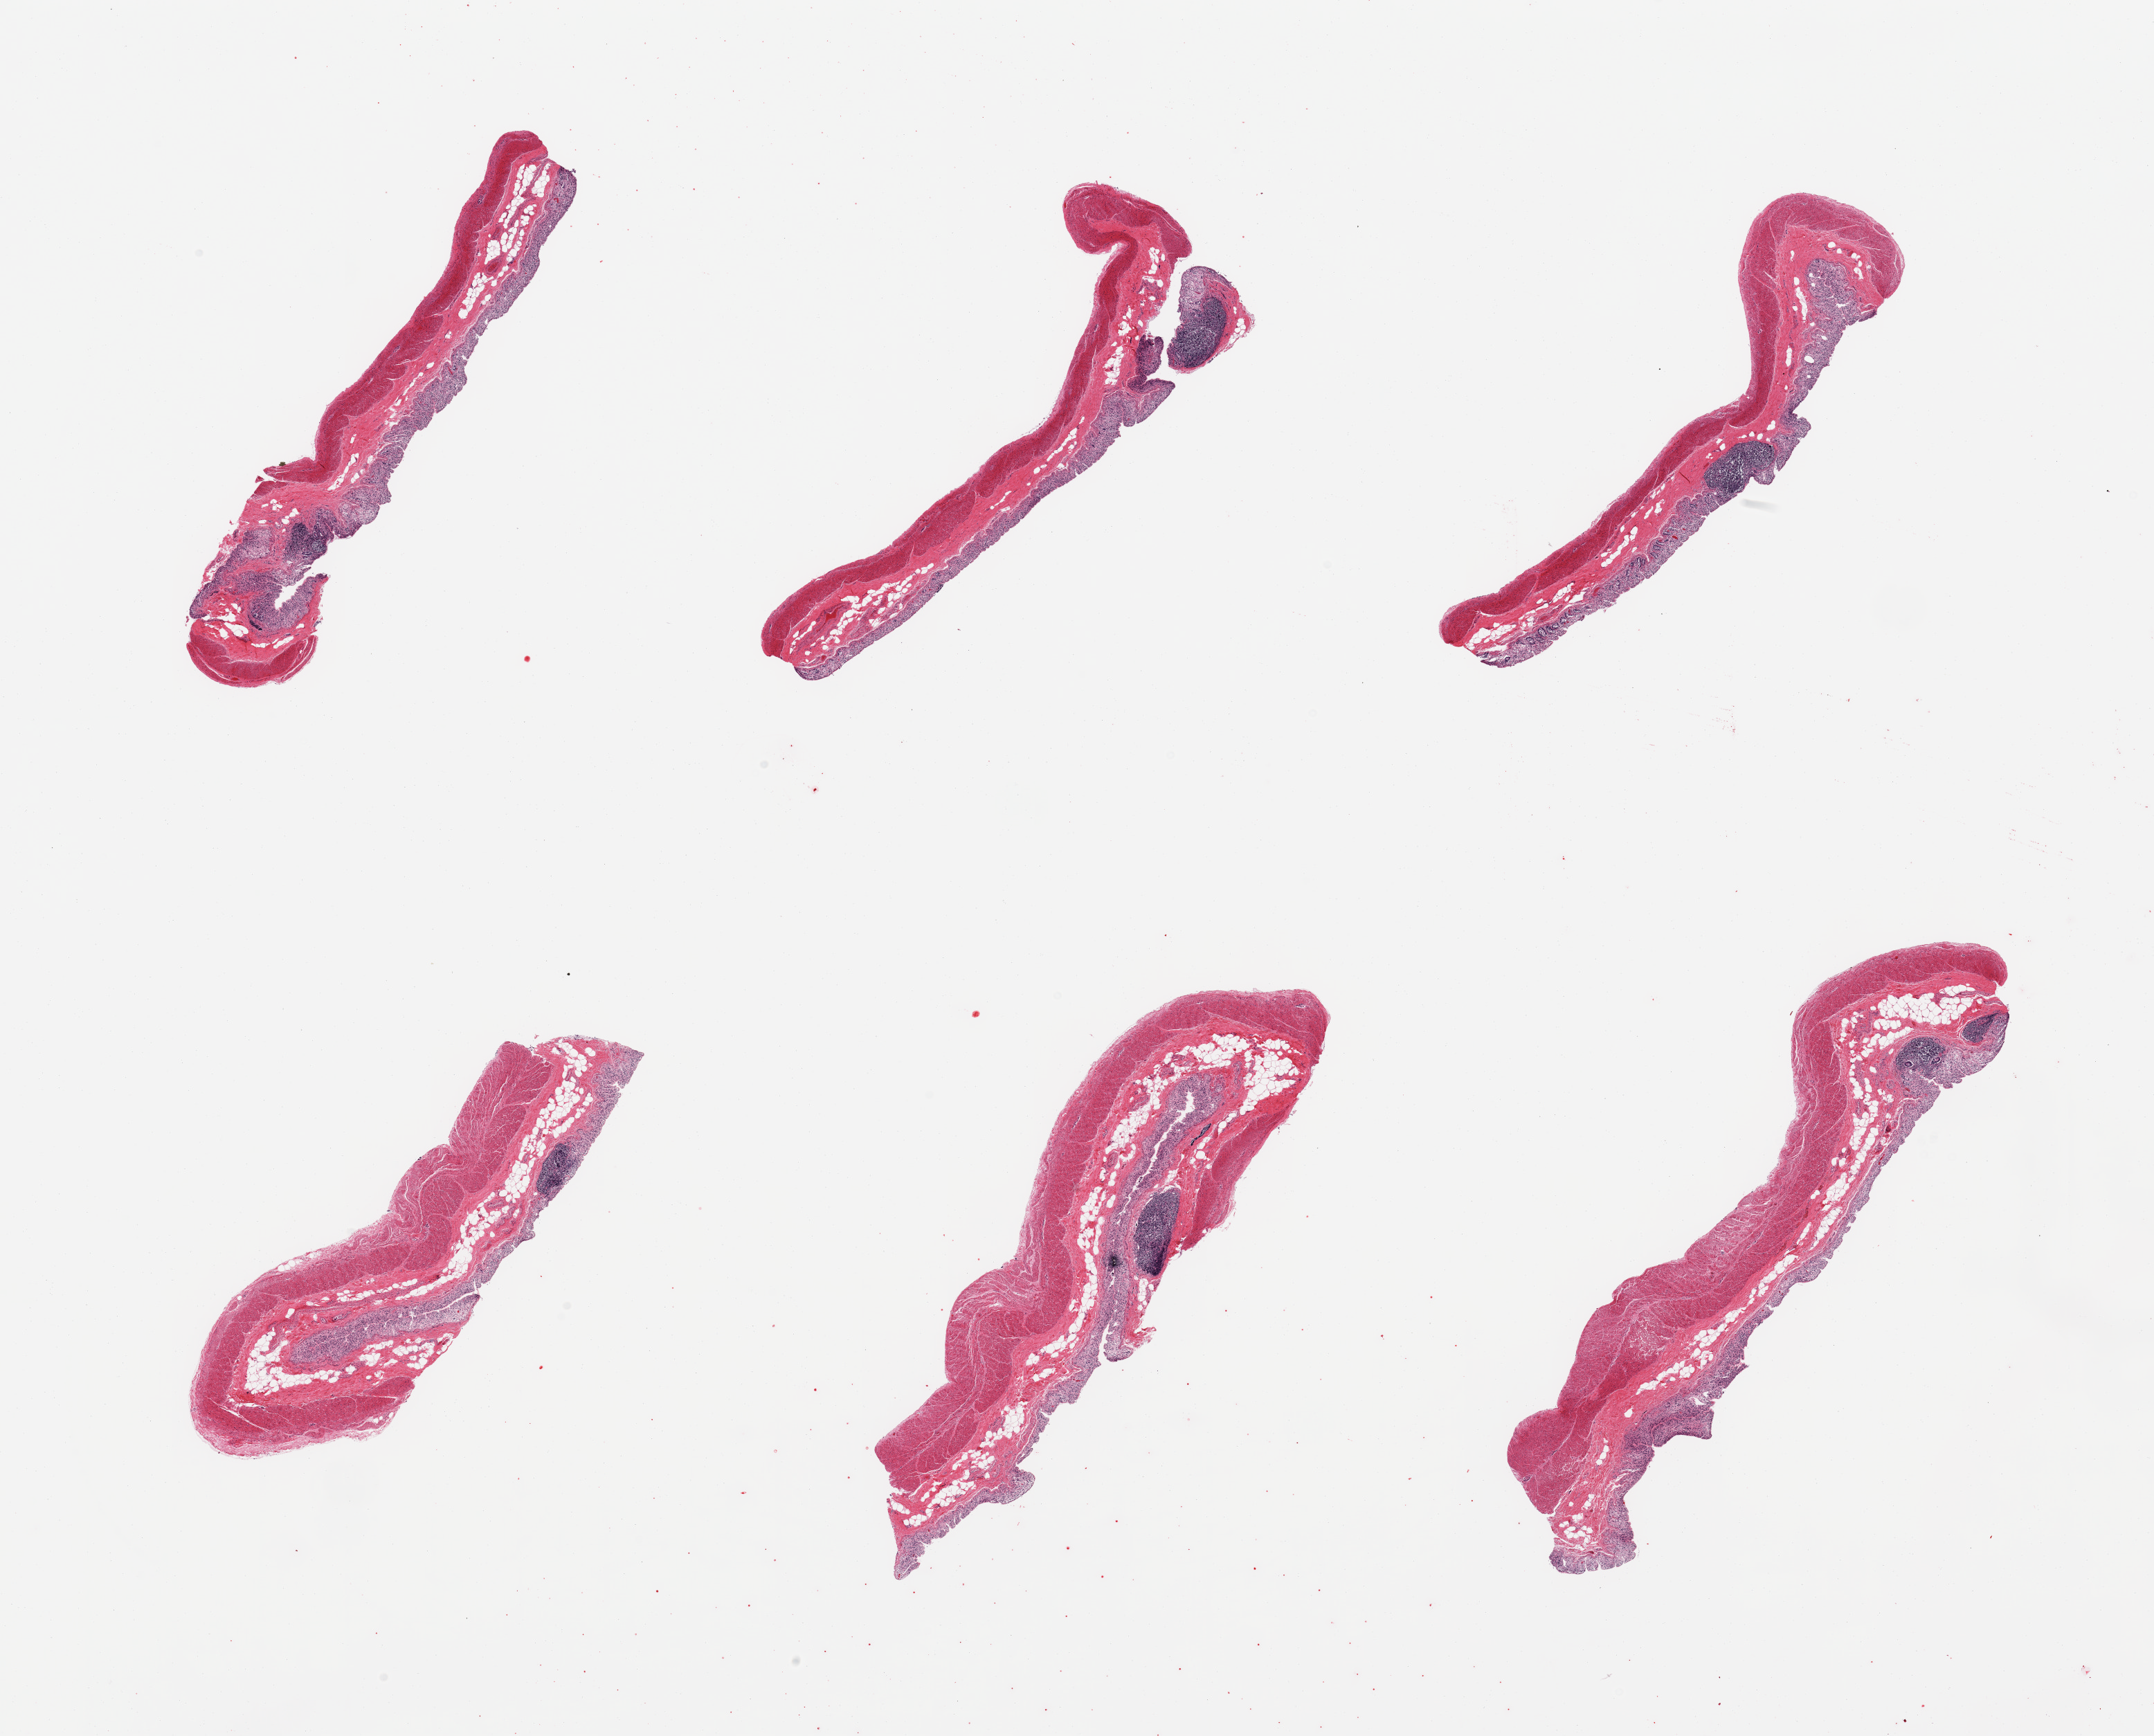
Whole-slide image, haematoxylin and eosin stain — low-resolution overview of the scanned area, about 24.6 x 19.8 mm (slide scanned at 20x). PAXgene-fixed paraffin-embedded (PFPE) section. Target tissue: transverse colon. Donor tissue sample. Male donor.
* reviewer comment on this tissue sample: 6 pieces; mucosa autolyzed, muscularis propria preserved; aggregates of lymphocytes